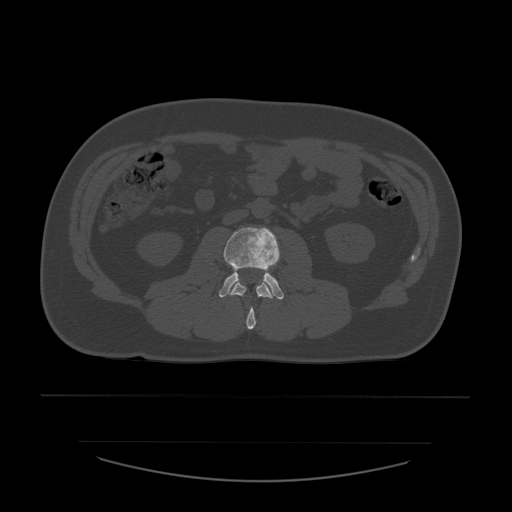
CT including the spine, one axial slice; position 184 of 532 along the scan axis; reconstruction kernel STANDARD; 120 kVp; bone window (W 1800 / L 400 HU); 1.25 mm slice thickness; 512 × 512 image matrix, field of view 441 × 441 mm. Patient age 44 years. Case-level facts recorded for this patient, not image findings: primary cancer: soft tissue sarcoma.
Structures marked on this image (semi-automatically segmented with operator editing):
- L2 vertebra: bounding box [x1, y1, x2, y2] px = [230, 282, 274, 330]
- L3 vertebra: [219, 227, 285, 300]